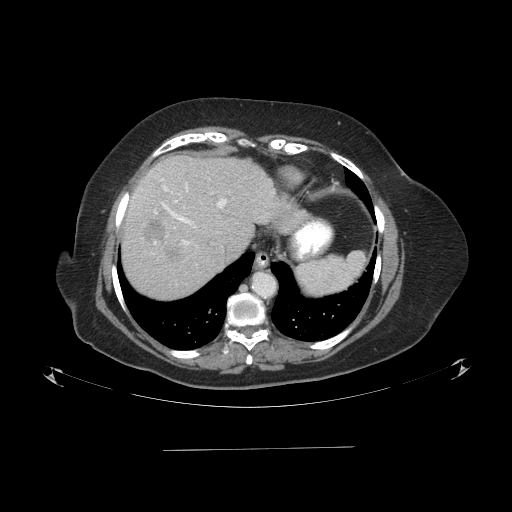
Contrast-enhanced abdominal CT (liver protocol), one axial slice; position 74 of 103 along the scan axis; 120 kVp; one of 2 acquisitions stored at this slice position; soft-tissue window (W 400 / L 40 HU); 2.5 mm slice thickness; 512 × 512 image matrix. From the clinical record (not read from this slice): diagnosis: hepatocellular carcinoma (patient treated with transarterial chemoembolisation; whether this scan precedes or follows treatment is not stated here); TNM stage (as recorded): Stage-IIIA; Child-Pugh class: A; tumour nodularity: multinodular.
Outlined on this slice (semi-automatically segmented with operator editing):
- liver parenchyma outside the tumour (the mass and vessels are separate outlines, so this box may not span the whole liver): bounding box <122,154,304,298> (left, top, right, bottom; pixels)
- mass: <142,220,182,262>
- liver vessels: <134,179,227,245>